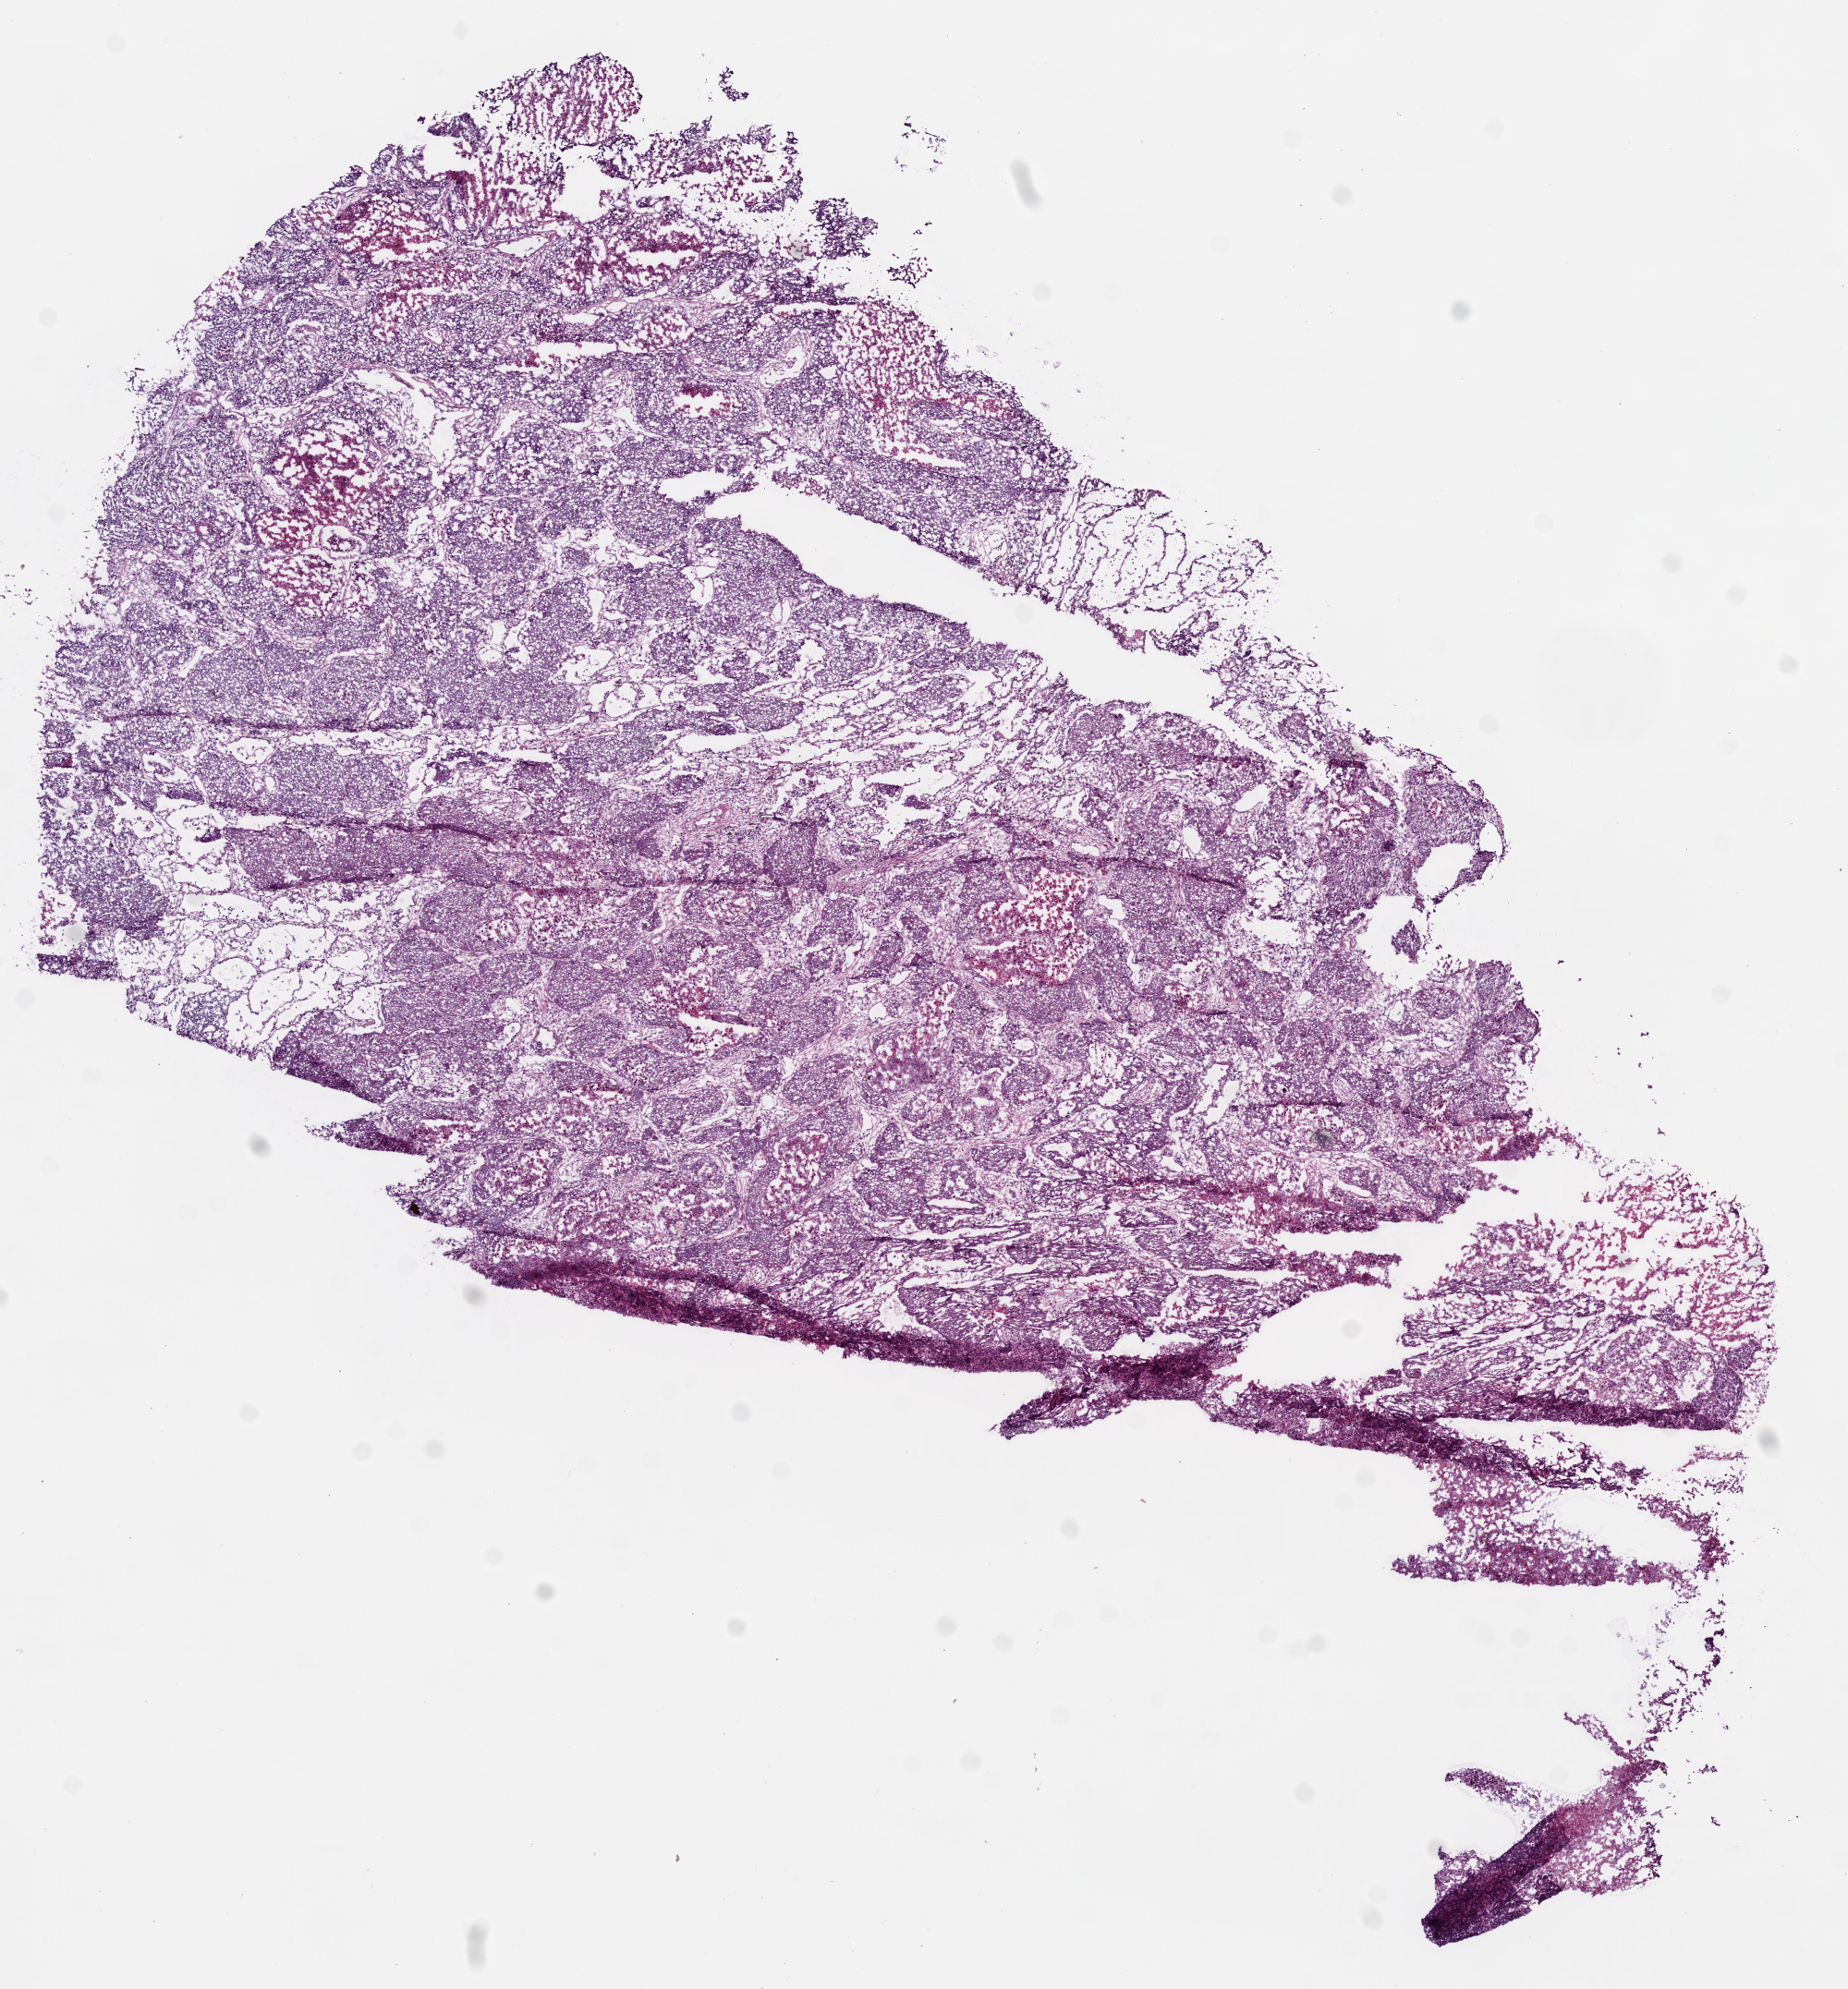
Digitized H&E tissue section (whole slide), shown as a low-resolution overview of the whole scanned area (about 8.0 x 8.6 mm, from a 20x scan). Frozen section from the bottom of the tissue portion. Lung, primary tumour sample. Patient: male, age at initial diagnosis 57 years. Composition of this section per pathologist review: tumour cells 75%, tumour nuclei 65%, normal cells 0%, stromal cells 15%, necrosis 10%.
TNM: T2 N2 M0. AJCC pathologic stage: IIIA. Pathologic diagnosis: Squamous cell carcinoma, NOS (lower lobe, lung).